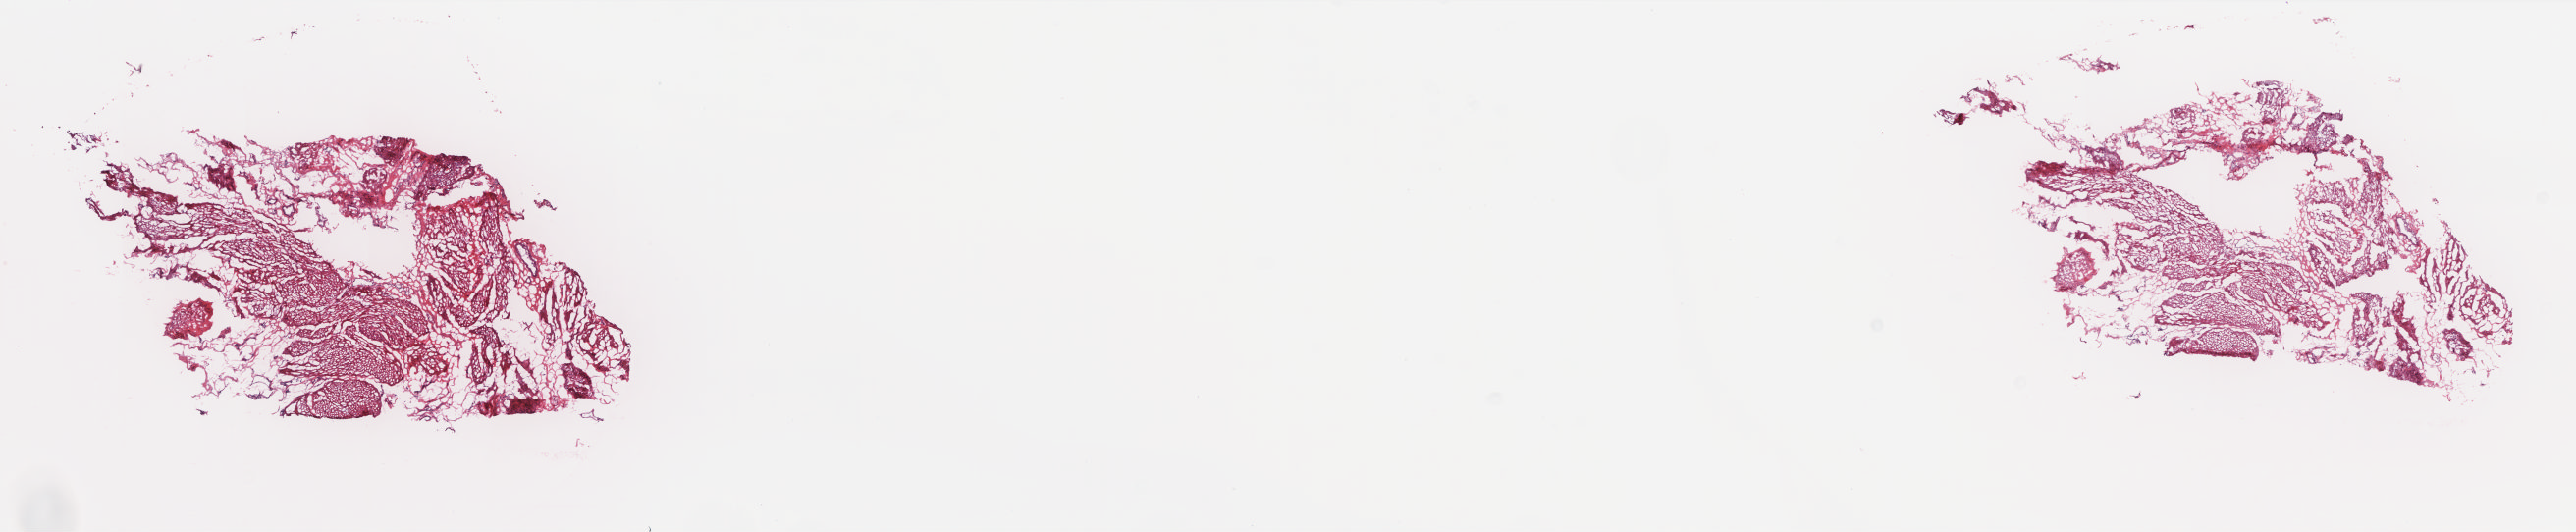
Digitized H&E tissue section (whole slide) — whole scanned area (about 21.0 x 4.3 mm, slide scanned at 20x) shown as a low-resolution overview; frozen section; sample: solid tissue normal (non-tumour tissue), bladder. Male patient; age at initial diagnosis 85 years. Pathologist review of this section (percent, as recorded): tumour cells 0%, tumour nuclei 0%.
This section: solid tissue normal sample (biorepository sample class). Patient diagnosis: Transitional cell carcinoma.